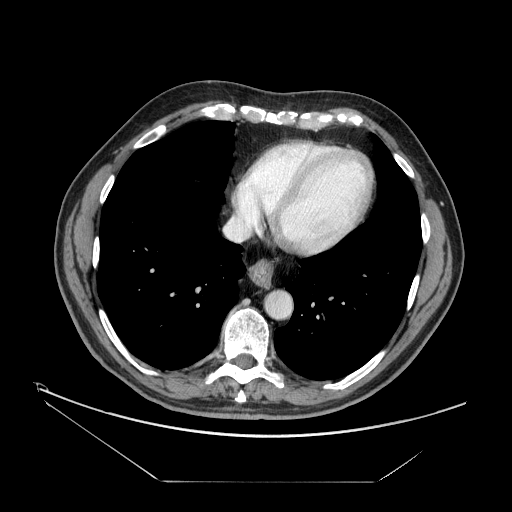
Contrast-enhanced abdominal CT, one axial slice; slice 157 of 161 in the series (ordered by position); intravenous contrast given; soft-tissue window (W 400 / L 40 HU); 2.5 mm slice thickness; 512 × 512 image matrix, field of view 440 × 440 mm. Male patient, age 65 years. Case-level facts recorded for this patient, not image findings: diagnosis: colorectal cancer liver metastases, imaged before liver resection; multiple liver metastases: yes; largest metastasis: 4.2 cm; disease in both lobes: yes.
Outlined on this slice (expert manual segmentation):
- hepatic veins: bounding box (x1, y1, x2, y2) in pixels: (224, 161, 266, 242)